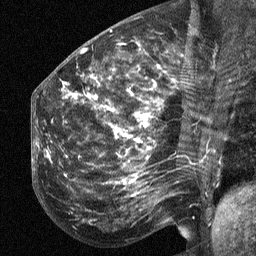
Breast MRI (dynamic contrast-enhanced), one sagittal slice; slice 26 of 64 in the series (ordered by position); dynamic contrast-enhanced study with each time point stored as its own series, time point 2 of 3 at this slice position (early post-contrast, ordered by acquisition time); 1.5 T; TE 4.8 ms, TR 27 ms; 2.3 mm slice thickness; 256 × 256 image matrix, field of view 200 × 200 mm. Patient: female, 50 years. From the clinical record (not read from this slice): setting: breast cancer imaged before/during neoadjuvant chemotherapy; receptor status: HER2-positive.
Outlined on this slice (semi-automatically segmented with operator editing):
- analysis volume of interest (the breast-tissue region the enhancement analysis was run in; not a lesion): bounding box <53,64,211,218> (left, top, right, bottom; pixels)
- tumour enhancement mask (voxels above the 90 % enhancement threshold inside the analysis volume of interest): <66,76,150,181>